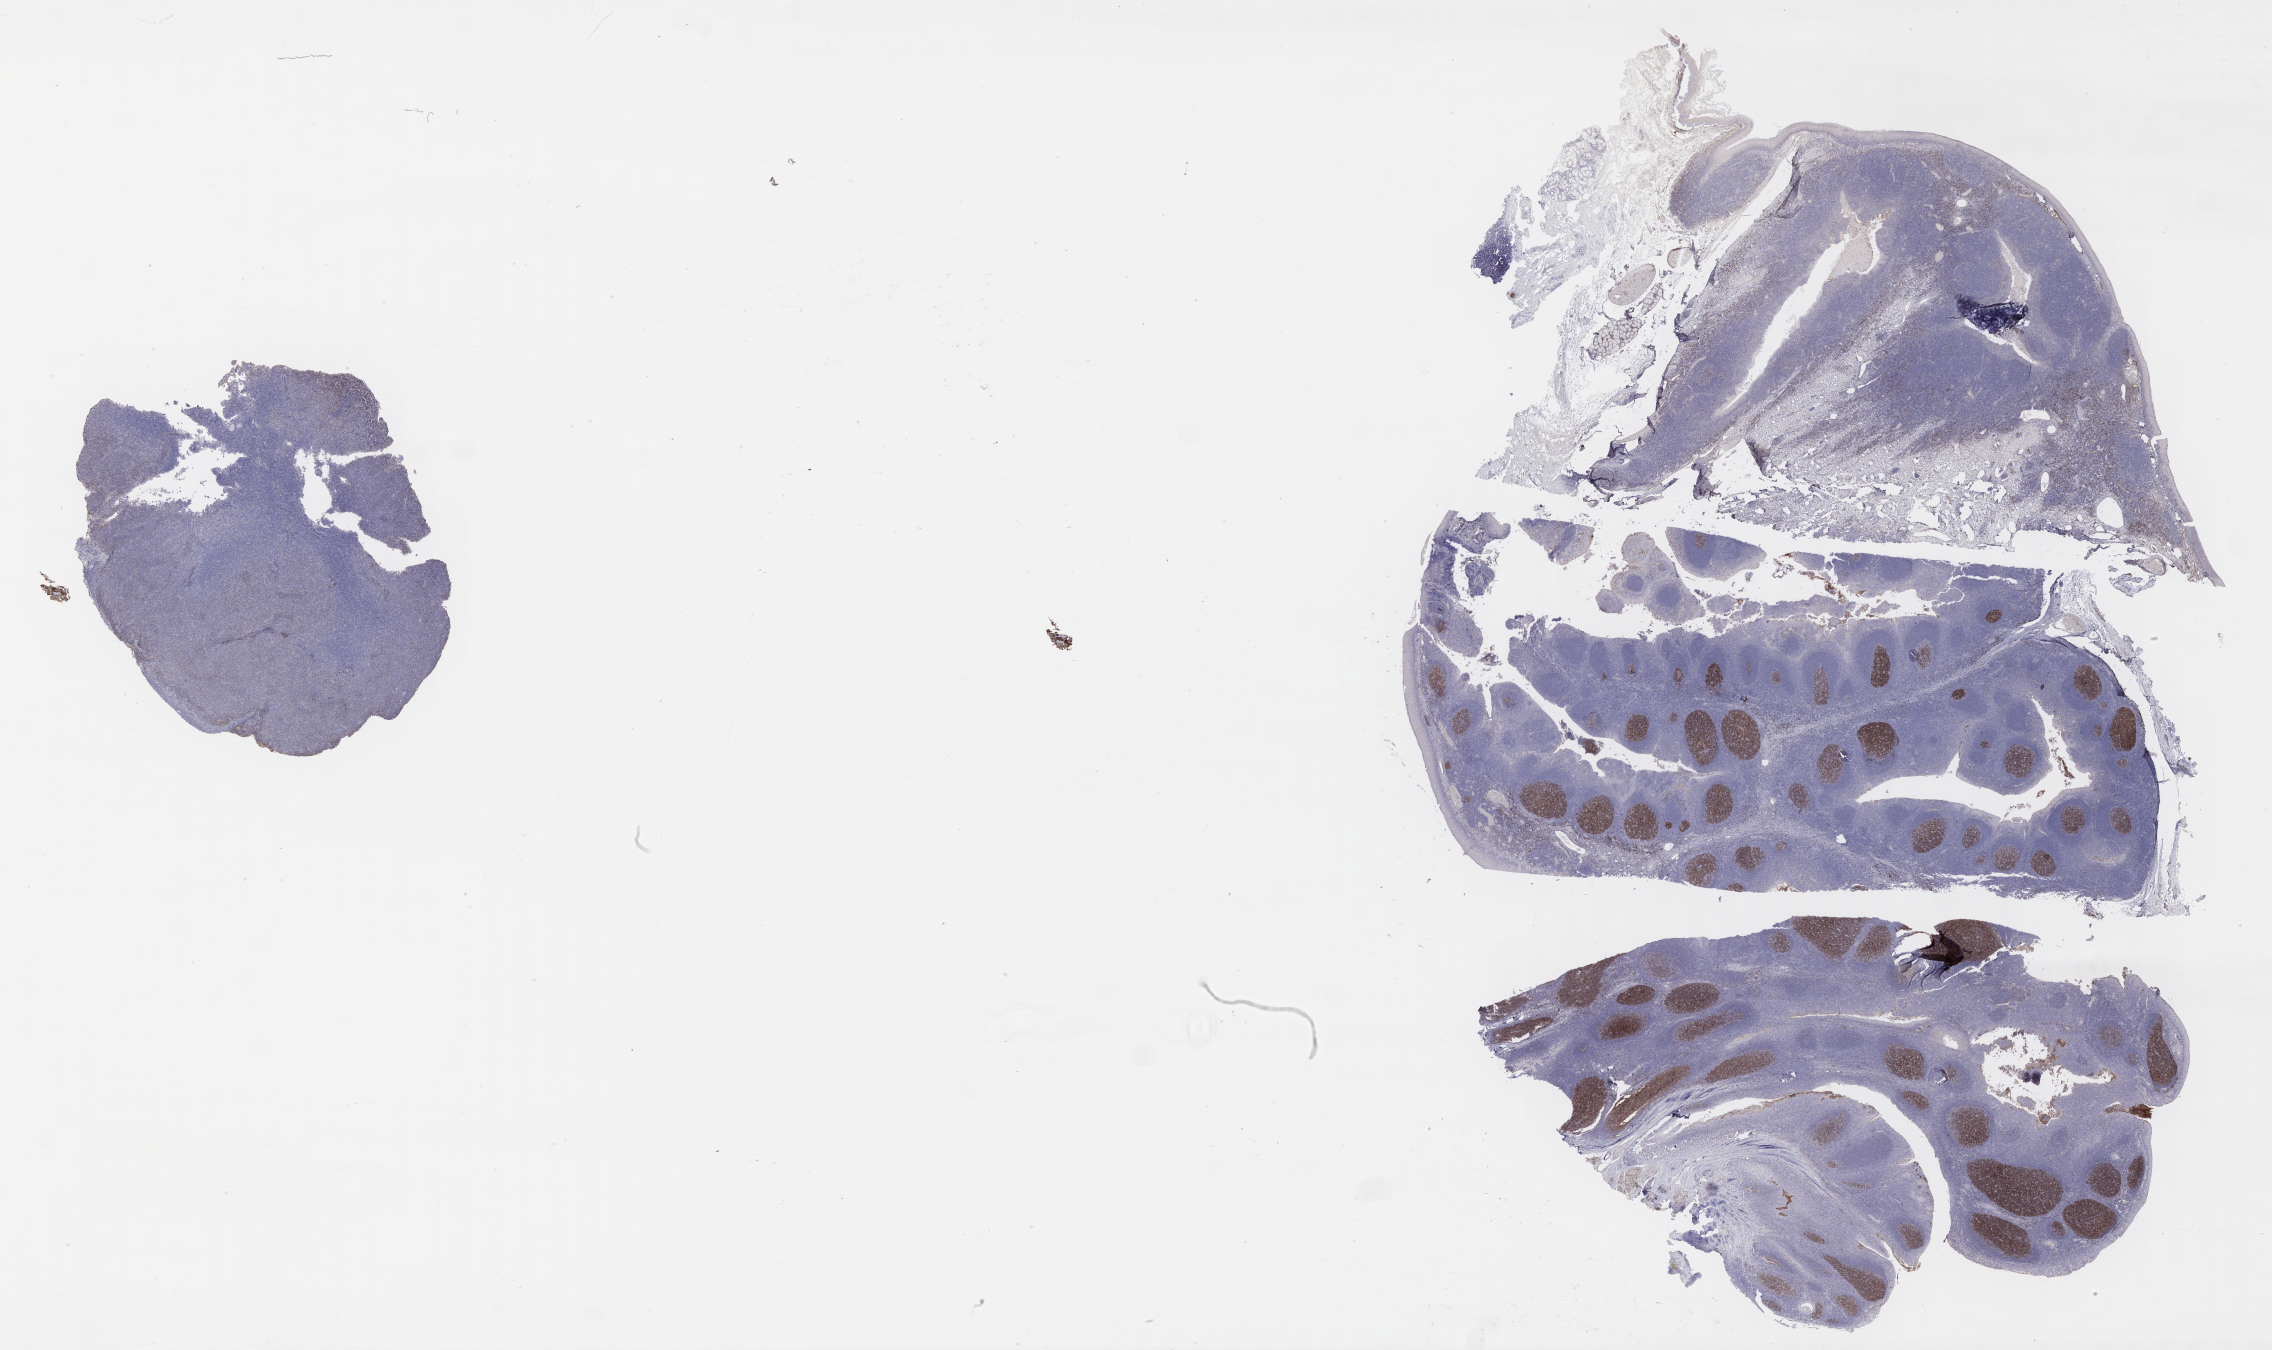
Whole-slide image, immunohistochemical stain for CD10, low-resolution overview of the scanned area, about 36.7 x 21.8 mm, specimen: tumor tissue, site: liver. Patient: male, age 46 years.
Diagnosis: Diffuse large B-cell lymphoma, NOS.